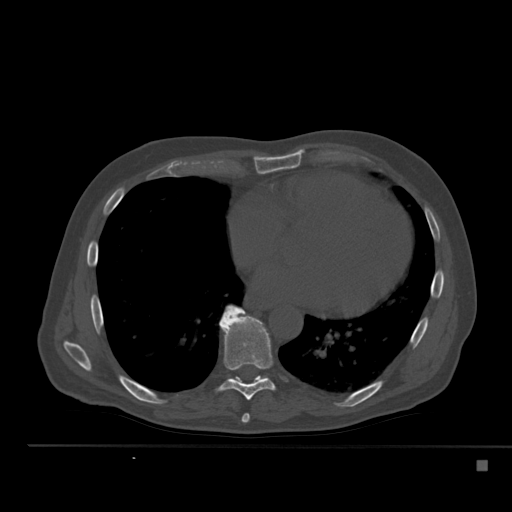
CT including the spine, one axial slice. Position 306 of 517 along the scan axis. 120 kVp. Bone window (W 1800 / L 400 HU). 512 × 512 image matrix. Male patient, age 70 years. From the clinical record (not read from this slice): primary cancer: renal; vertebrae with lytic lesions (as recorded): T4, T6, T10, T12, L3, L4, L5.
Structures marked on this image (semi-automatically segmented with operator editing):
- T7 vertebra: bounding box (x1, y1, x2, y2) in pixels: (241, 414, 250, 423)
- T8 vertebra: (218, 305, 275, 400)
- T9 vertebra: (230, 376, 263, 380)